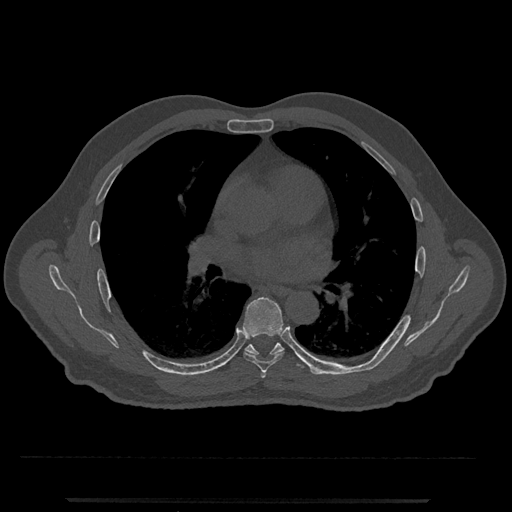
CT including the spine, one axial slice; position 718 of 797 along the scan axis; 120 kVp; bone window (W 1800 / L 400 HU); 0.5 mm slice thickness; 512 × 512 image matrix, field of view 419 × 419 mm. Male patient, age 63 years. From the clinical record (not read from this slice): primary cancer: prostate.
Annotated regions visible in this slice (semi-automatically segmented with operator editing):
- T5 vertebra: bounding box <261,372,266,378> (left, top, right, bottom; pixels)
- T6 vertebra: <243,296,284,373>
- T7 vertebra: <245,341,320,375>